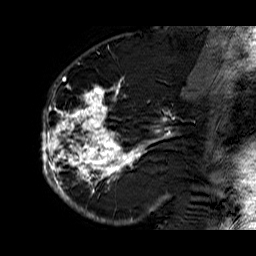
Breast MRI (dynamic contrast-enhanced), one sagittal slice. Position 37 of 60 along the scan axis. Dynamic contrast-enhanced series, time point 2 of 6 at this slice position (early post-contrast). 1.5 T. TE 6.3 ms, TR 32.9 ms. 256 × 256 image matrix, field of view 200 × 200 mm. Female patient. Case-level facts recorded for this patient, not image findings: setting: breast cancer imaged before/during neoadjuvant chemotherapy; receptor status: HR-positive, HER2-negative.
Outlined on this slice (semi-automatically segmented with operator editing):
- analysis volume of interest (the breast-tissue region the enhancement analysis was run in; not a lesion): bounding box <40,74,176,210> (left, top, right, bottom; pixels)
- tumour enhancement mask (voxels above the 100 % enhancement threshold inside the analysis volume of interest): <41,74,171,210>